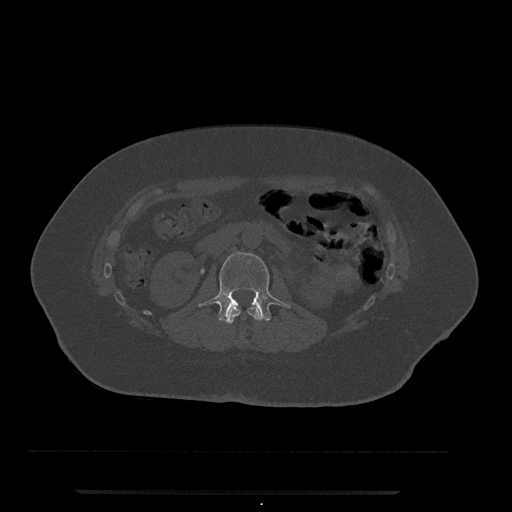
CT including the spine, one axial slice. Position 52 of 797 along the scan axis. Reconstruction kernel Br40s/3. 120 kVp. Bone window (W 1800 / L 400 HU). 512 × 512 image matrix, field of view 440 × 440 mm. Female patient, age 51 years. From the clinical record (not read from this slice): primary cancer: neuro.
Annotated regions visible in this slice (semi-automatic segmentation, software-assisted and operator-edited):
- L1 vertebra: bounding box [x1, y1, x2, y2] px = [225, 306, 261, 340]
- L2 vertebra: [199, 251, 291, 322]